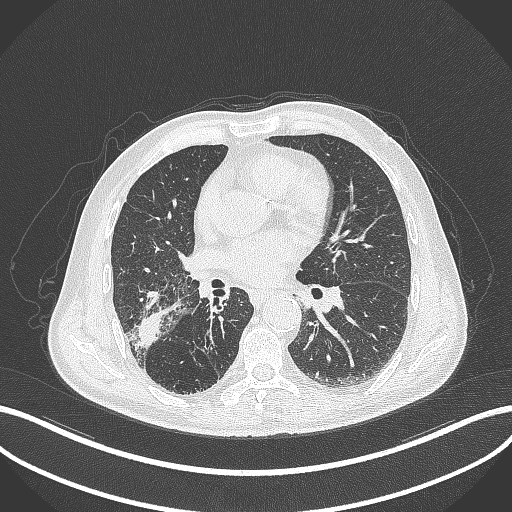
Chest CT, one axial slice. Position 208 of 429 along the scan axis. 120 kVp. Lung window (W 1500 / L -600 HU). 512 × 512 image matrix, field of view 400 × 400 mm. Male patient, age 72 years. Case-level facts recorded for this patient, not image findings: clinical TNM (as recorded): T3 N2 M0.
Outlined on this slice (rectangle marked by the reading radiologist):
- lung tumour (recorded histology: adenocarcinoma): bounding box (x1, y1, x2, y2) in pixels: (132, 308, 159, 347)